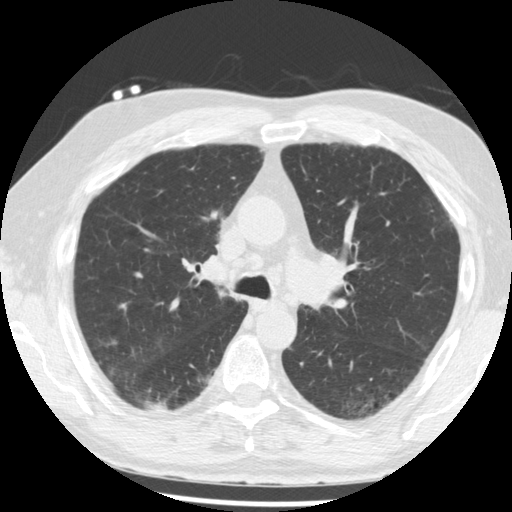
Low-dose screening chest CT, one axial slice; position 138 of 221 along the scan axis; reconstruction kernel STANDARD; lung window (W 1500 / L -600 HU); 2.5 mm slice thickness; 512 × 512 image matrix, field of view 350 × 350 mm.
Outlined on this slice (manually delineated by an expert):
- lesion 1 (tumor, lower lobe of right lung): bounding box [x1, y1, x2, y2] px = [145, 401, 177, 412]